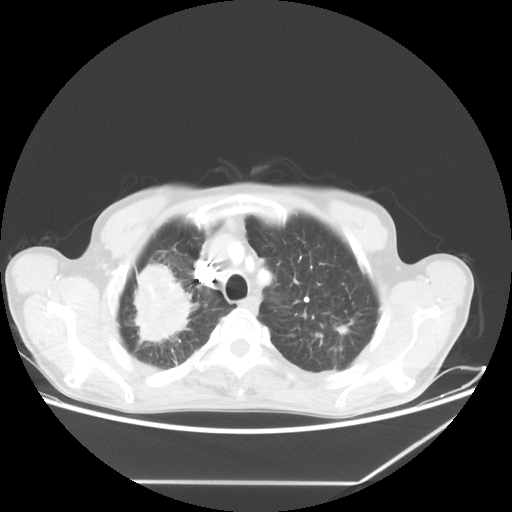
Chest CT, one axial slice. Position 52 of 65 along the scan axis. Reconstruction kernel STANDARD. Lung window (W 1500 / L -600 HU). 5 mm slice thickness. 512 × 512 image matrix. Patient: male, 68 years. Case-level facts recorded for this patient, not image findings: clinical TNM (as recorded): T3 N3 M0.
Outlined on this slice (bounding box drawn by a radiologist):
- lung tumour (recorded histology: adenocarcinoma): bounding box <120,258,187,353> (left, top, right, bottom; pixels)